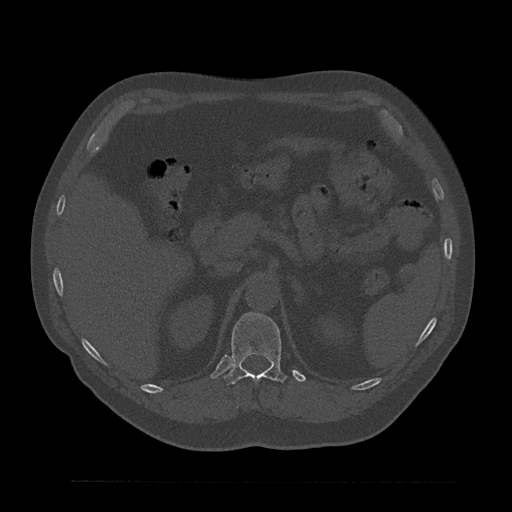
CT including the spine, one axial slice. Position 232 of 797 along the scan axis. Reconstruction kernel Br40s/3. 120 kVp. Bone window (W 1800 / L 400 HU). 0.5 mm slice thickness. 512 × 512 image matrix, field of view 430 × 430 mm. Patient: male, 61 years. From the clinical record (not read from this slice): primary cancer: prostate.
Structures marked on this image (semi-automatic segmentation, software-assisted and operator-edited):
- T12 vertebra: bounding box <224,312,287,385> (left, top, right, bottom; pixels)